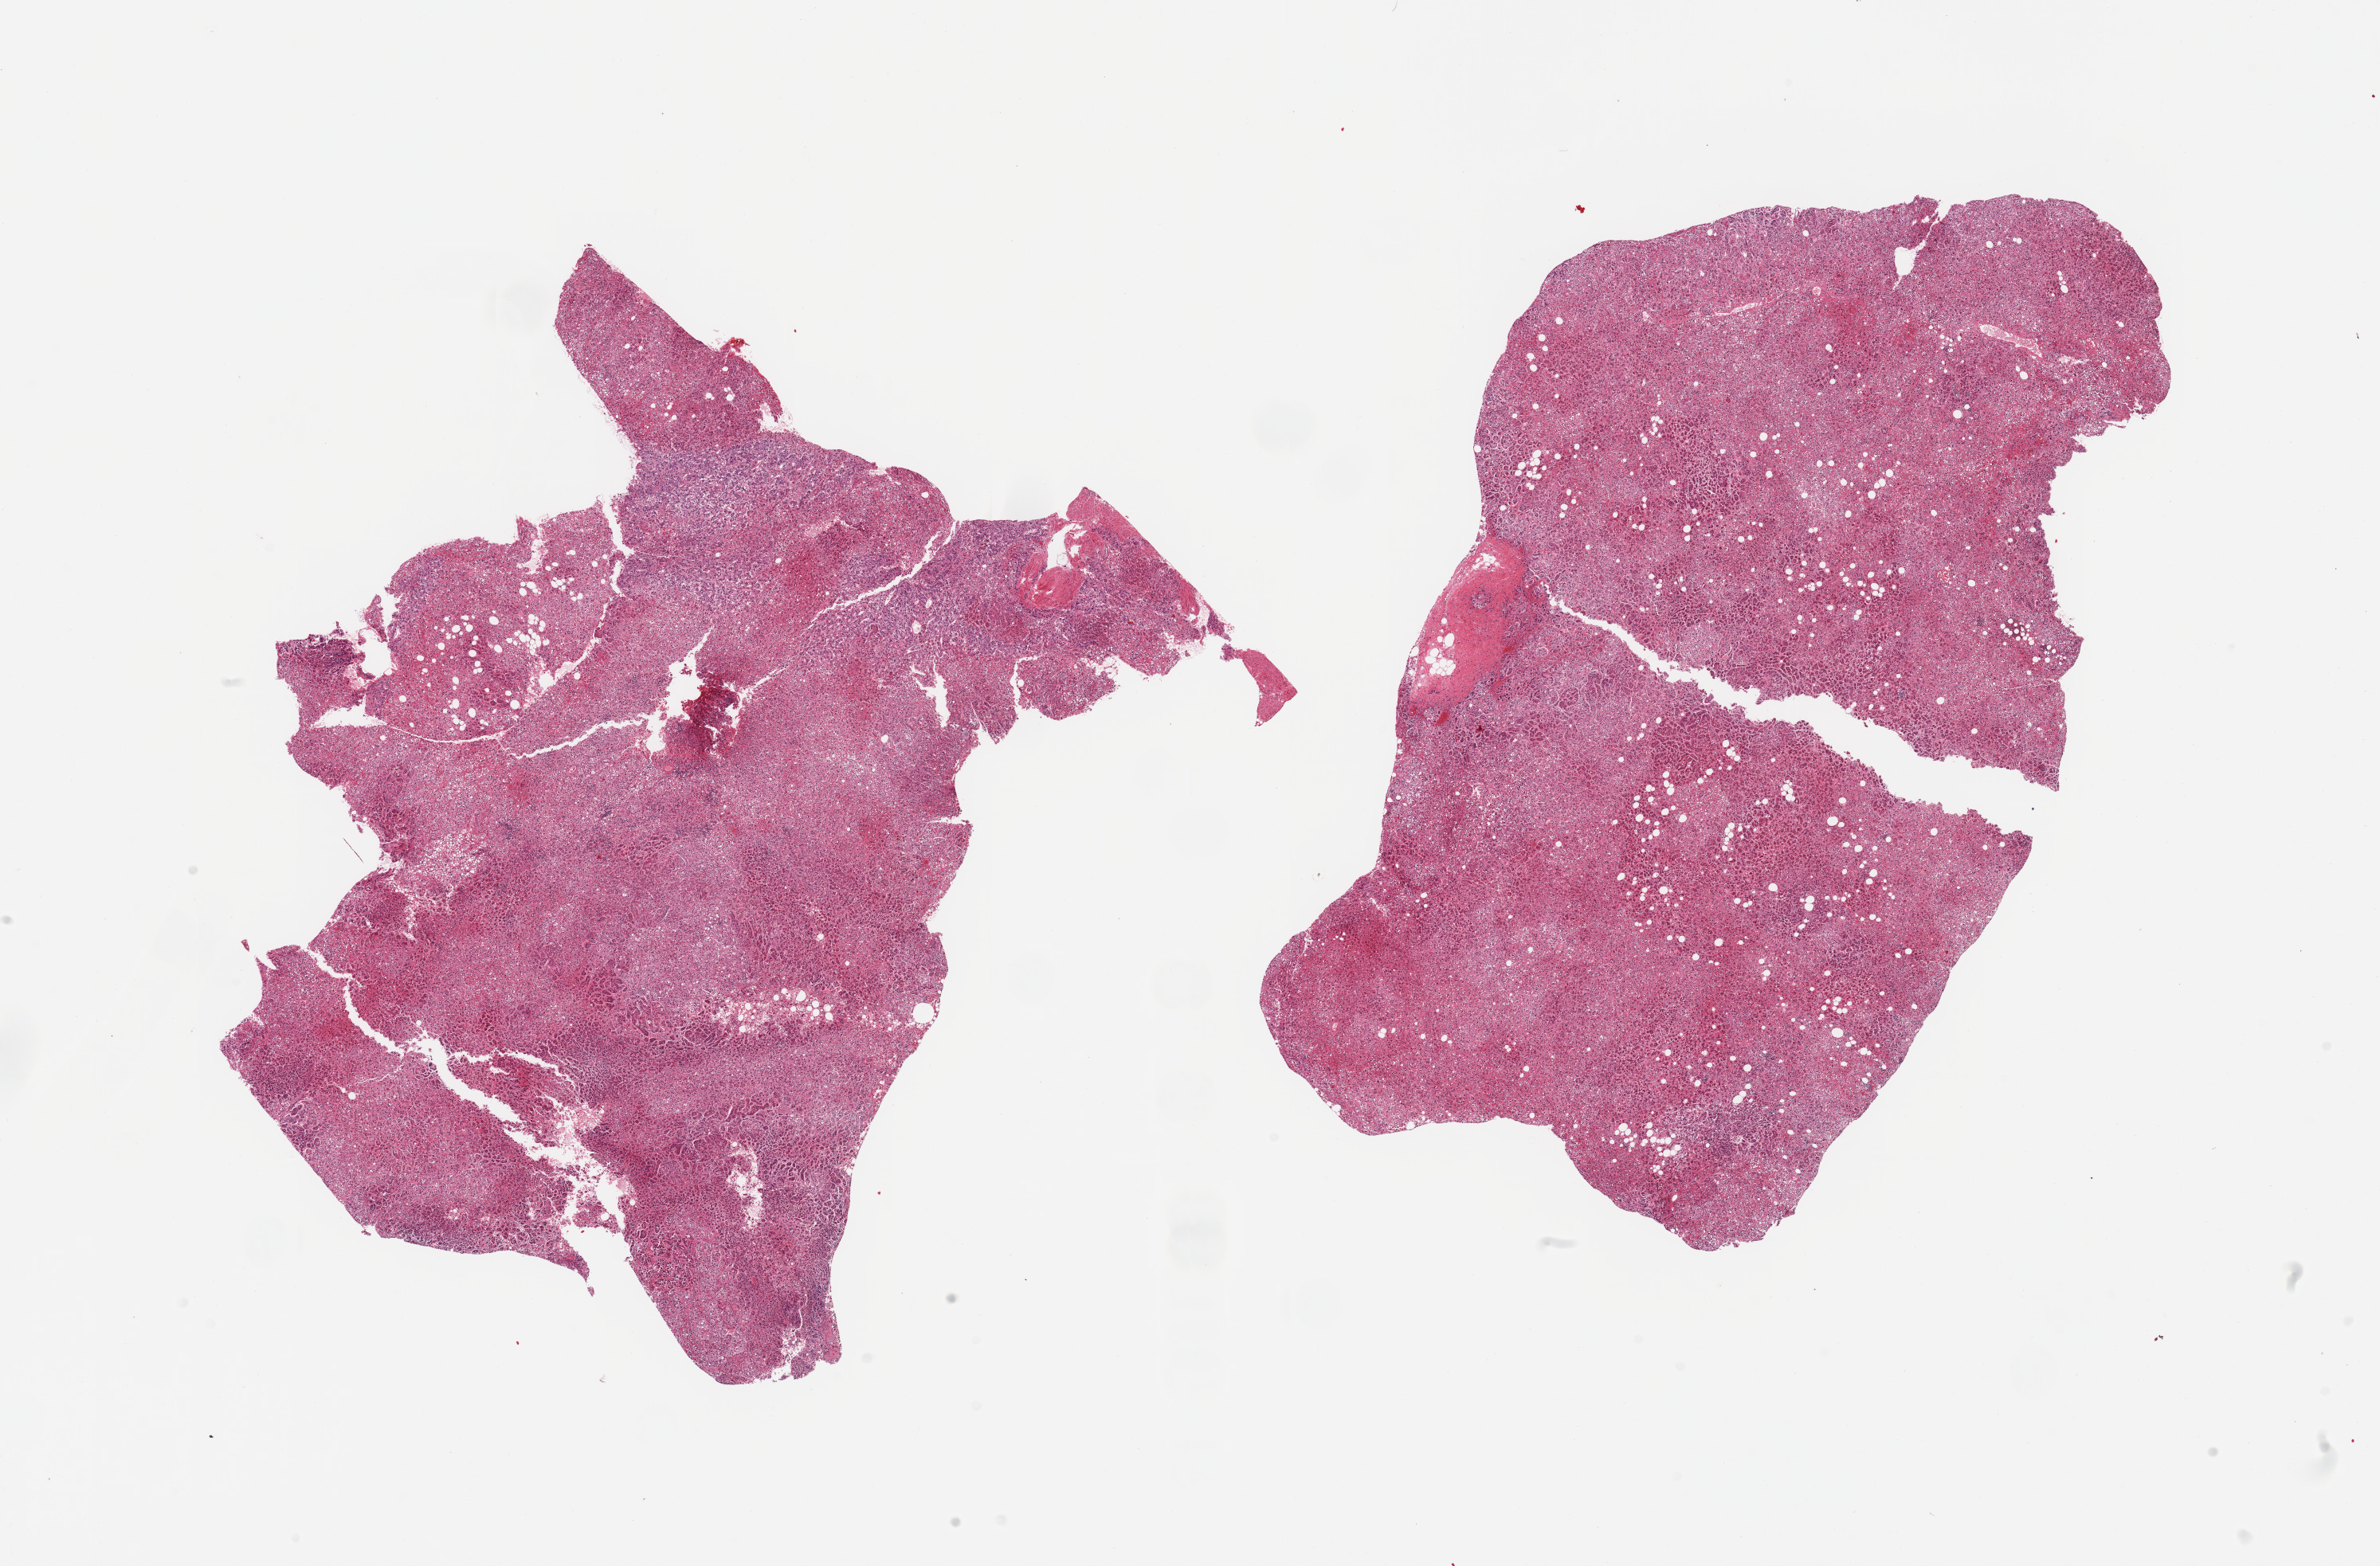
Whole-slide image, hematoxylin and eosin (H&E) stain — a low-resolution overview of the entire scanned area, about 23.6 x 15.6 mm (slide scanned at 20x); PAXgene-fixed paraffin-embedded (PFPE) section; sampled site (target tissue): adrenal gland; tissue donor sample. Donor sex: male.
Review note (as recorded): 2 pieces, cortex, no abnormalities.